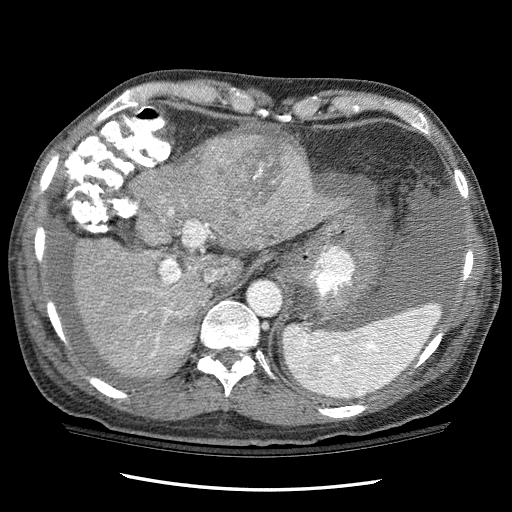
Contrast-enhanced abdominal CT (liver protocol), one axial slice; position 81 of 114 along the scan axis; reconstruction kernel STANDARD; 120 kVp; one of 3 acquisitions stored at this slice position; soft-tissue window (W 400 / L 40 HU); 2.5 mm slice thickness; 512 × 512 image matrix. From the clinical record (not read from this slice): diagnosis: hepatocellular carcinoma (patient treated with transarterial chemoembolisation; whether this scan precedes or follows treatment is not stated here); TNM stage (as recorded): Stage-I; Child-Pugh class: C; tumour differentiation: well differentiated; tumour nodularity: uninodular.
Structures marked on this image (semi-automatic segmentation, software-assisted and operator-edited):
- abdominal aorta: bounding box (x1, y1, x2, y2) in pixels: (248, 282, 281, 316)
- liver parenchyma outside the tumour (the mass and vessels are separate outlines, so this box may not span the whole liver): (63, 139, 334, 376)
- mass: (192, 126, 318, 241)
- liver vessels: (134, 271, 217, 358)